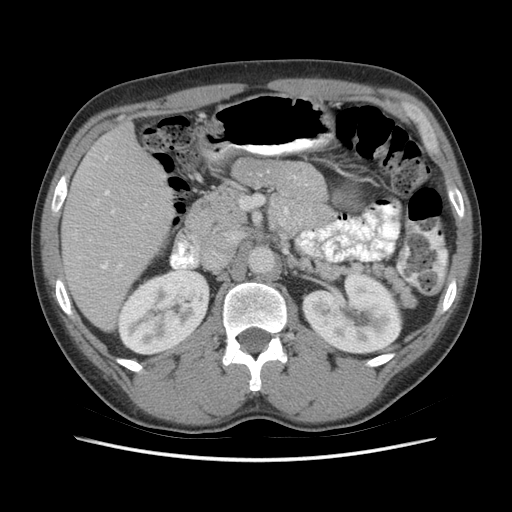
Contrast-enhanced abdominal CT (liver protocol), one axial slice; position 27 of 73 along the scan axis; reconstruction kernel STANDARD; soft-tissue window (W 400 / L 40 HU); 512 × 512 image matrix, field of view 360 × 360 mm. Case-level facts recorded for this patient, not image findings: diagnosis: hepatocellular carcinoma (patient treated with transarterial chemoembolisation; whether this scan precedes or follows treatment is not stated here); TNM stage (as recorded): Stage-IIIA; Child-Pugh class: A; tumour nodularity: multinodular; tumour size: 6.6 cm.
Outlined on this slice (semi-automatic segmentation, software-assisted and operator-edited):
- liver parenchyma outside the tumour (the mass and vessels are separate outlines, so this box may not span the whole liver): box from (x=62, y=124) to (x=172, y=330) px
- liver vessels: (x=101, y=157)–(x=122, y=269)